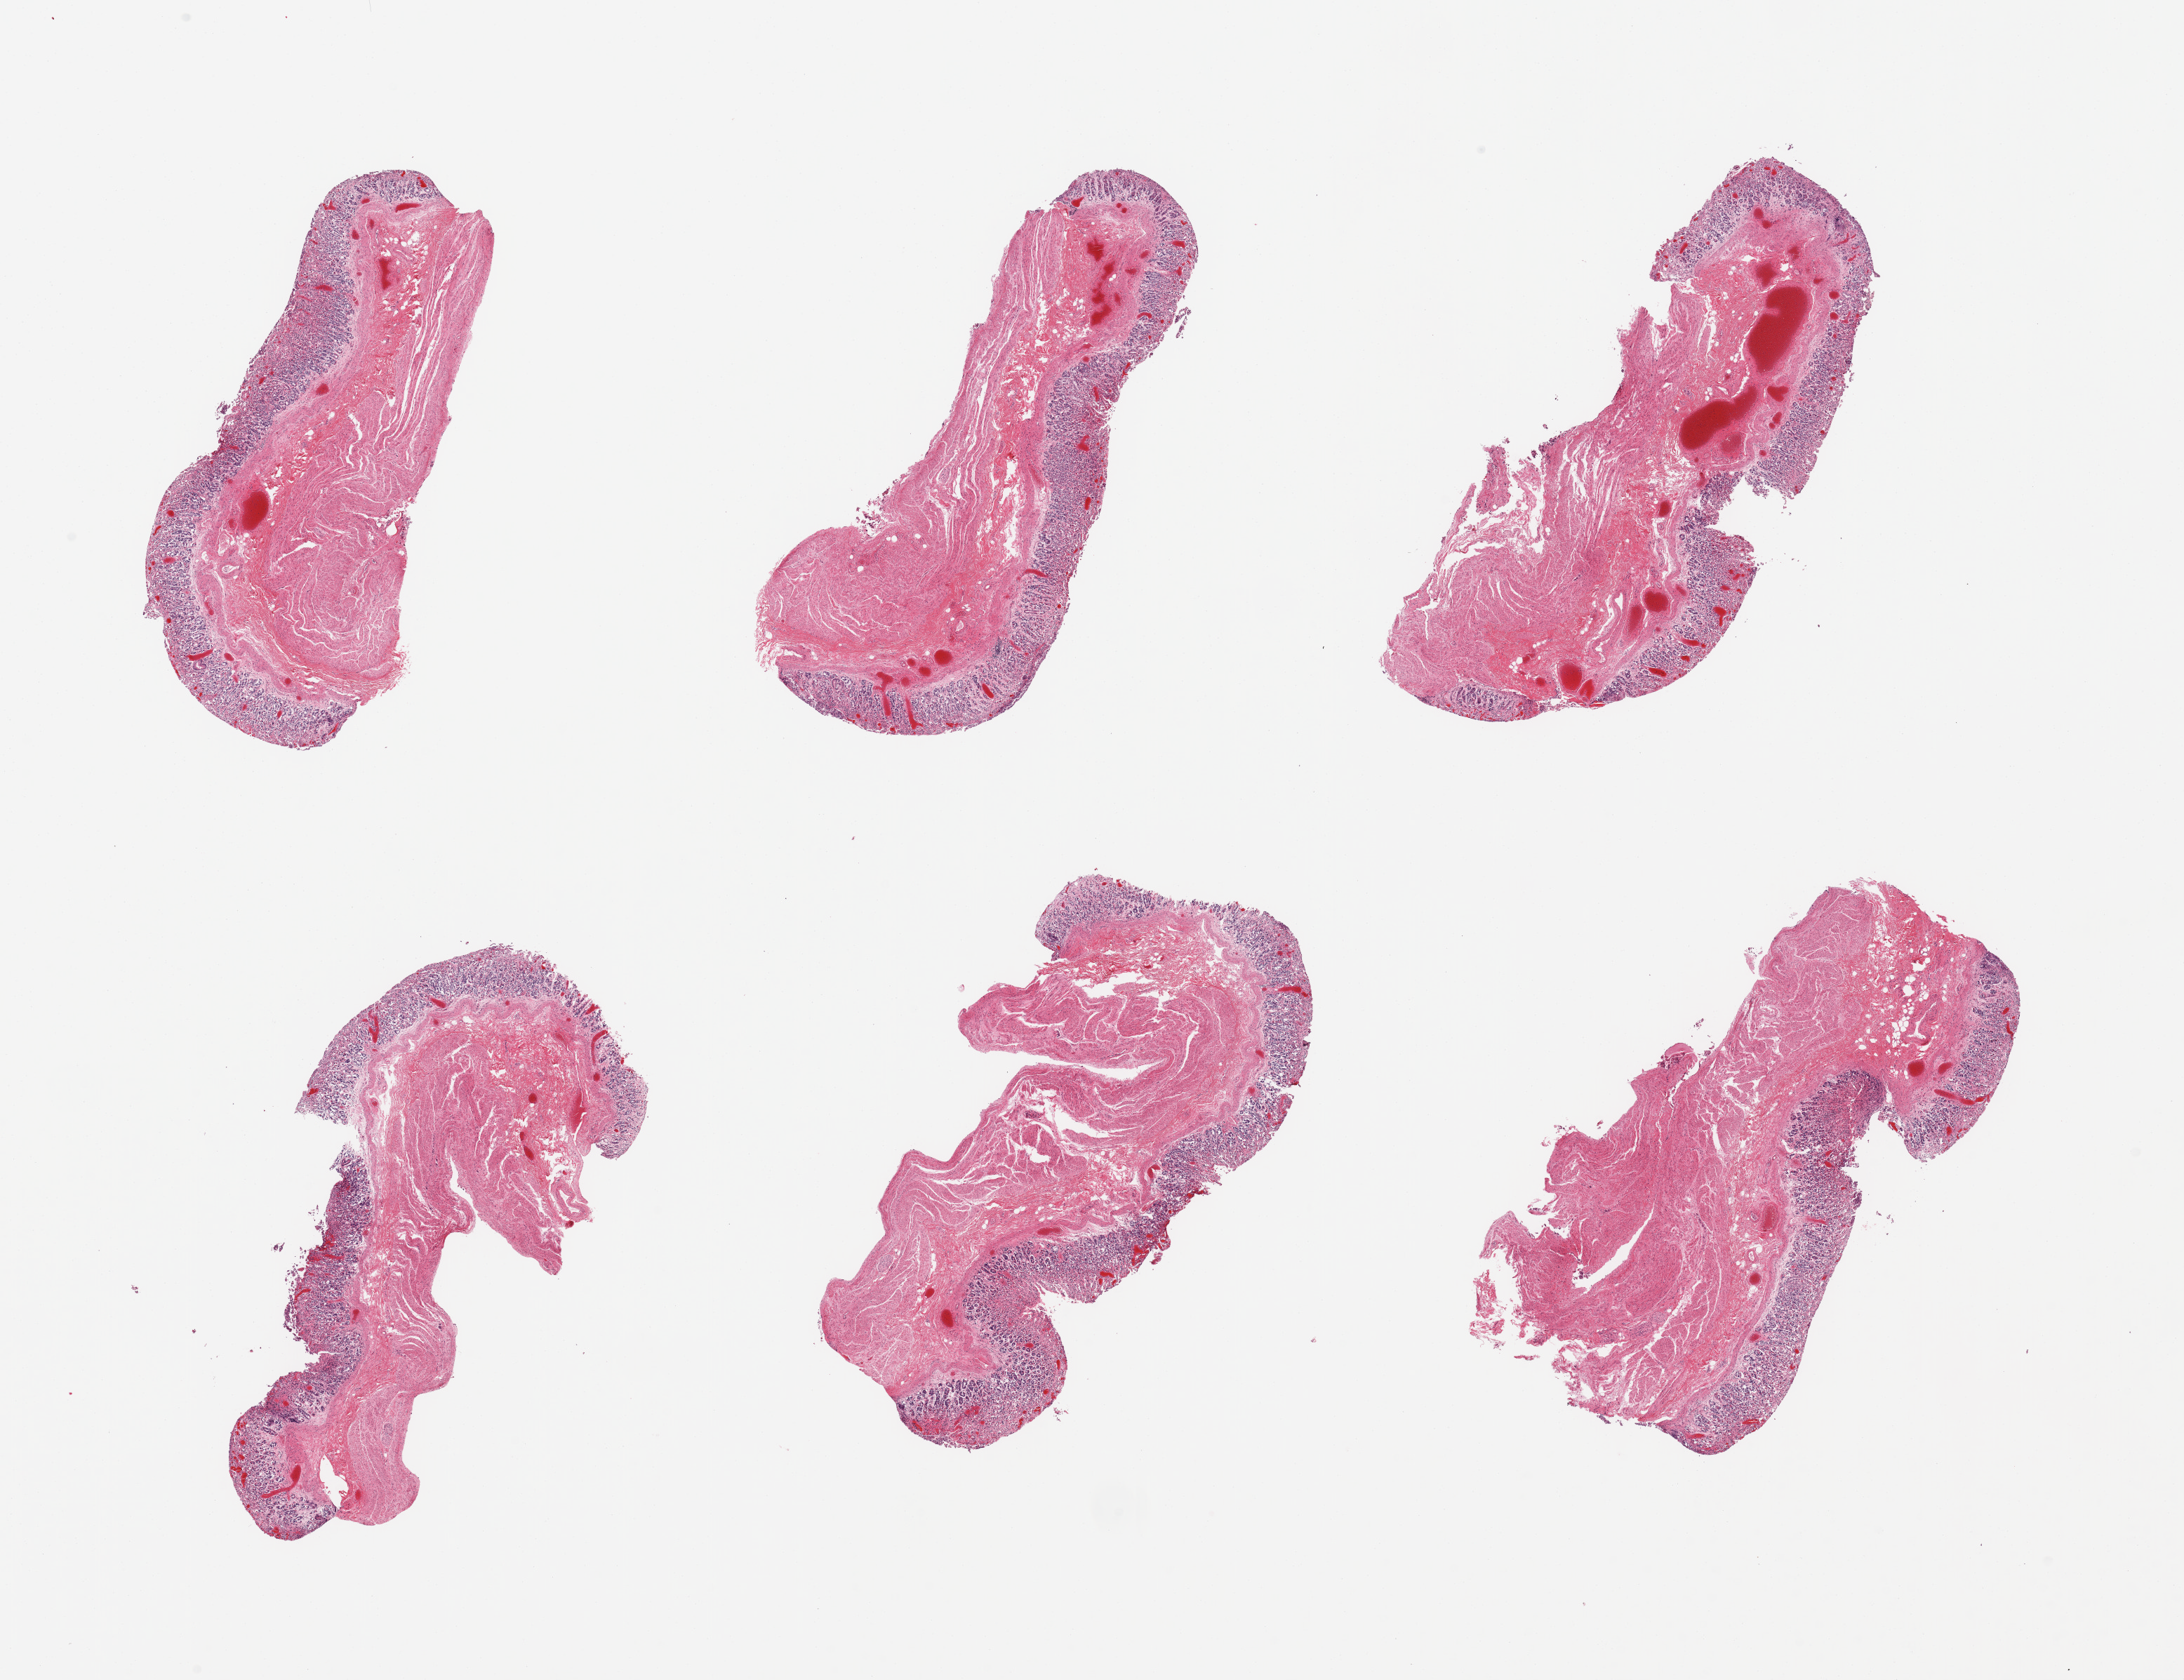
Hematoxylin and eosin (H&E) whole-slide image, whole scanned area (about 24.6 x 18.9 mm) shown as a low-resolution overview. PAXgene-fixed, paraffin-embedded tissue. Section of stomach (target tissue). Donor tissue sample.
Pathologist's review note for this sample: 6 pieces, glandular mucosa ~0.75mm thick,with moderate-advanced autolysis, , ~30% thickness.